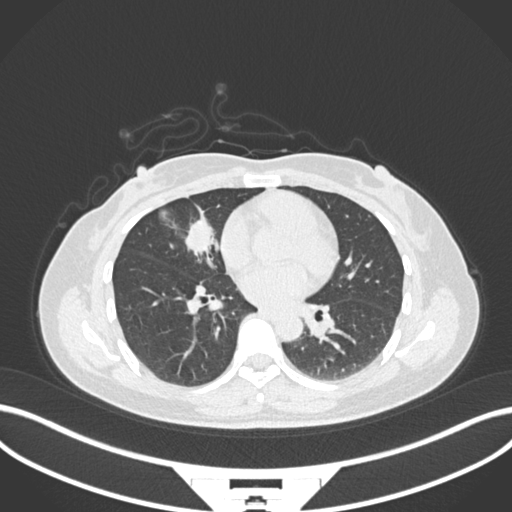
Chest CT, one axial slice. Slice 77 of 171 in the series (ordered by position). Lung window (W 1500 / L -600 HU). 1 mm slice thickness. 512 × 512 image matrix, field of view 400 × 400 mm. Patient: female, 43 years. Case-level facts recorded for this patient, not image findings: clinical TNM (as recorded): T1c N3 M1.
Structures marked on this image (bounding box drawn by a radiologist):
- lung tumour (recorded histology: adenocarcinoma): bounding box [x1, y1, x2, y2] px = [183, 214, 223, 268]